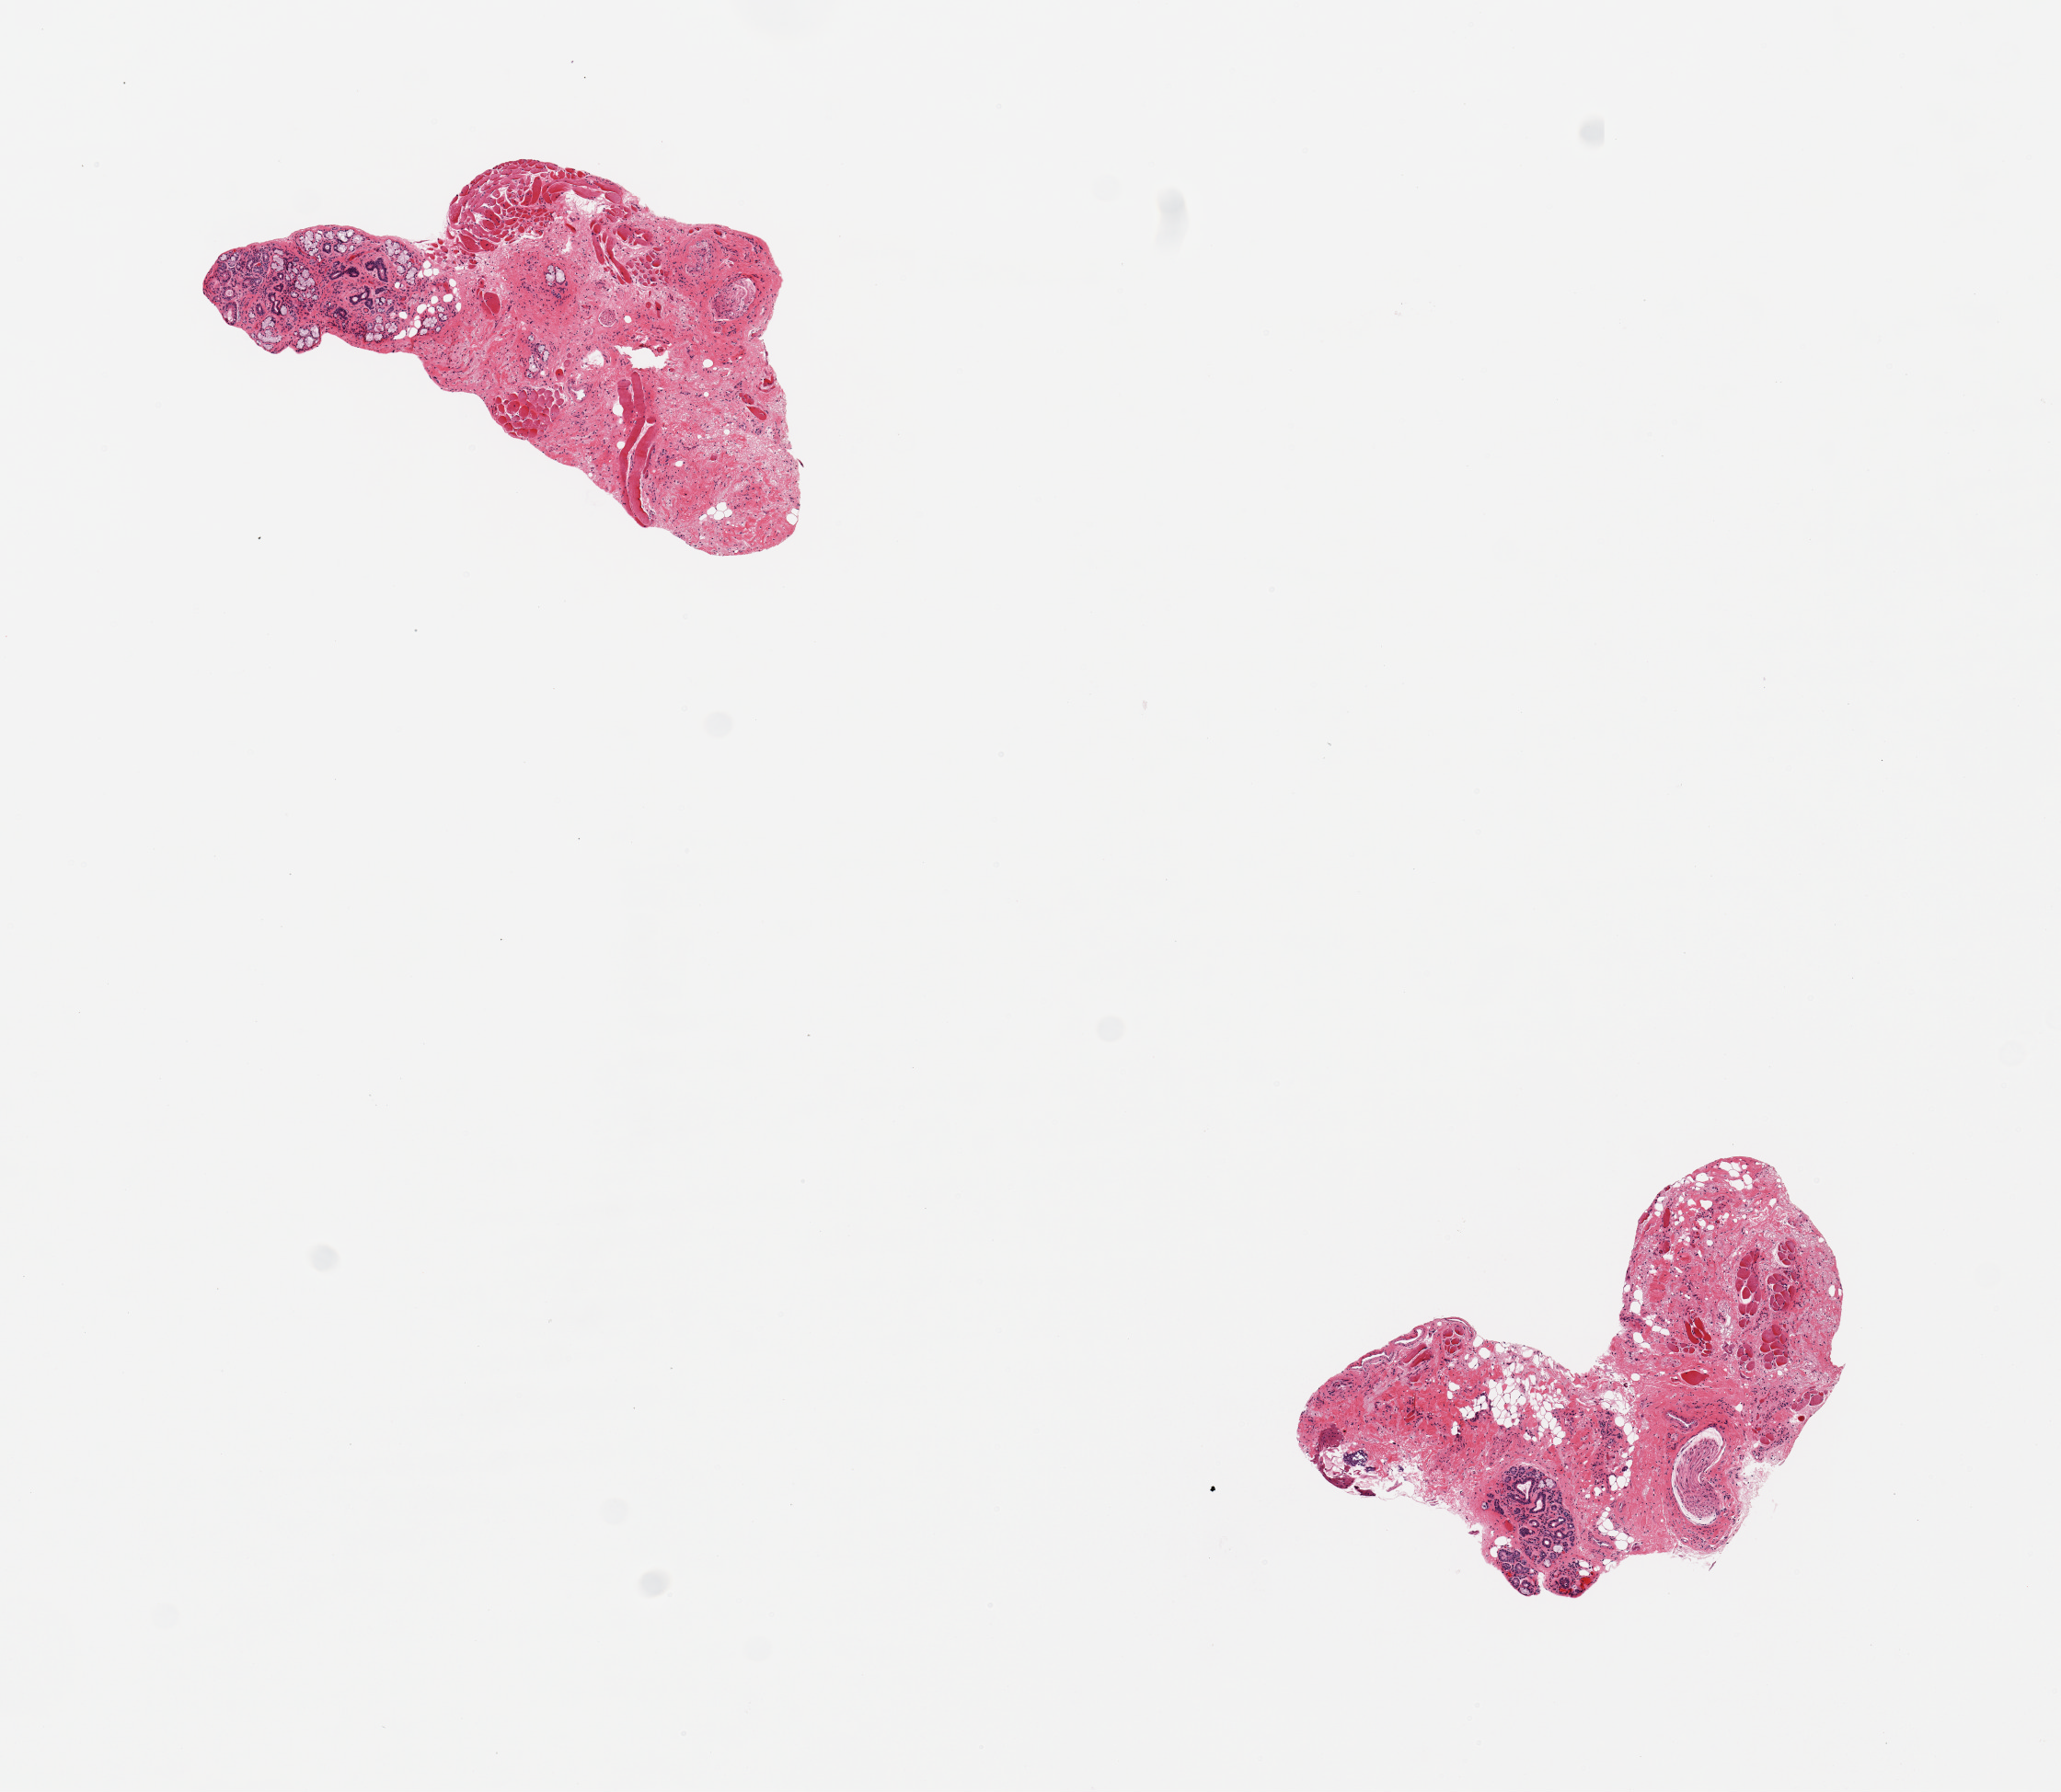
Digitized haematoxylin and eosin-stained section, brightfield, low-resolution overview of the scanned area, about 8.9 x 7.7 mm. Donor sex: male.
Specimen: PAXgene-fixed, paraffin-embedded tissue; section of minor salivary gland (target tissue); tissue donor sample.